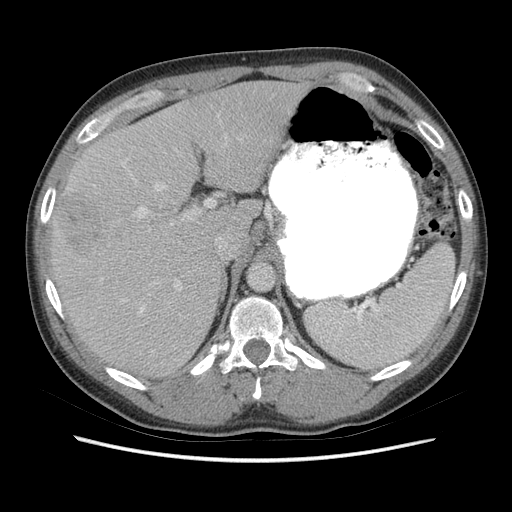
Contrast-enhanced abdominal CT (liver protocol), one axial slice; position 47 of 73 along the scan axis; reconstruction kernel STANDARD; soft-tissue window (W 400 / L 40 HU); 2.5 mm slice thickness; 512 × 512 image matrix, field of view 360 × 360 mm. From the clinical record (not read from this slice): diagnosis: hepatocellular carcinoma (patient treated with transarterial chemoembolisation; whether this scan precedes or follows treatment is not stated here); TNM stage (as recorded): Stage-IIIA; Child-Pugh class: A; tumour nodularity: multinodular.
Annotated regions visible in this slice (semi-automatically segmented with operator editing):
- liver parenchyma outside the tumour (the mass and vessels are separate outlines, so this box may not span the whole liver): bounding box [x1, y1, x2, y2] px = [50, 80, 308, 376]
- mass: [56, 191, 102, 258]
- liver vessels: [122, 162, 190, 313]